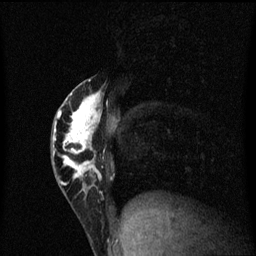
Breast MRI (dynamic contrast-enhanced), one sagittal slice. Slice 26 of 60 in the series (ordered by position). Dynamic contrast-enhanced series, image 2 of 3 at this slice position (ordered by acquisition). 1.5 T. TE 4.2 ms, TR 8.4 ms. 2 mm slice thickness. 256 × 256 image matrix. Female patient, age 40 years.
Outlined on this slice (semi-automatically segmented with operator editing):
- analysis volume of interest (the breast-tissue region the enhancement analysis was run in; not a lesion): bounding box [x1, y1, x2, y2] px = [52, 80, 109, 203]
- tumour enhancement mask (voxels above the 70 % enhancement threshold inside the analysis volume of interest): [54, 80, 103, 193]